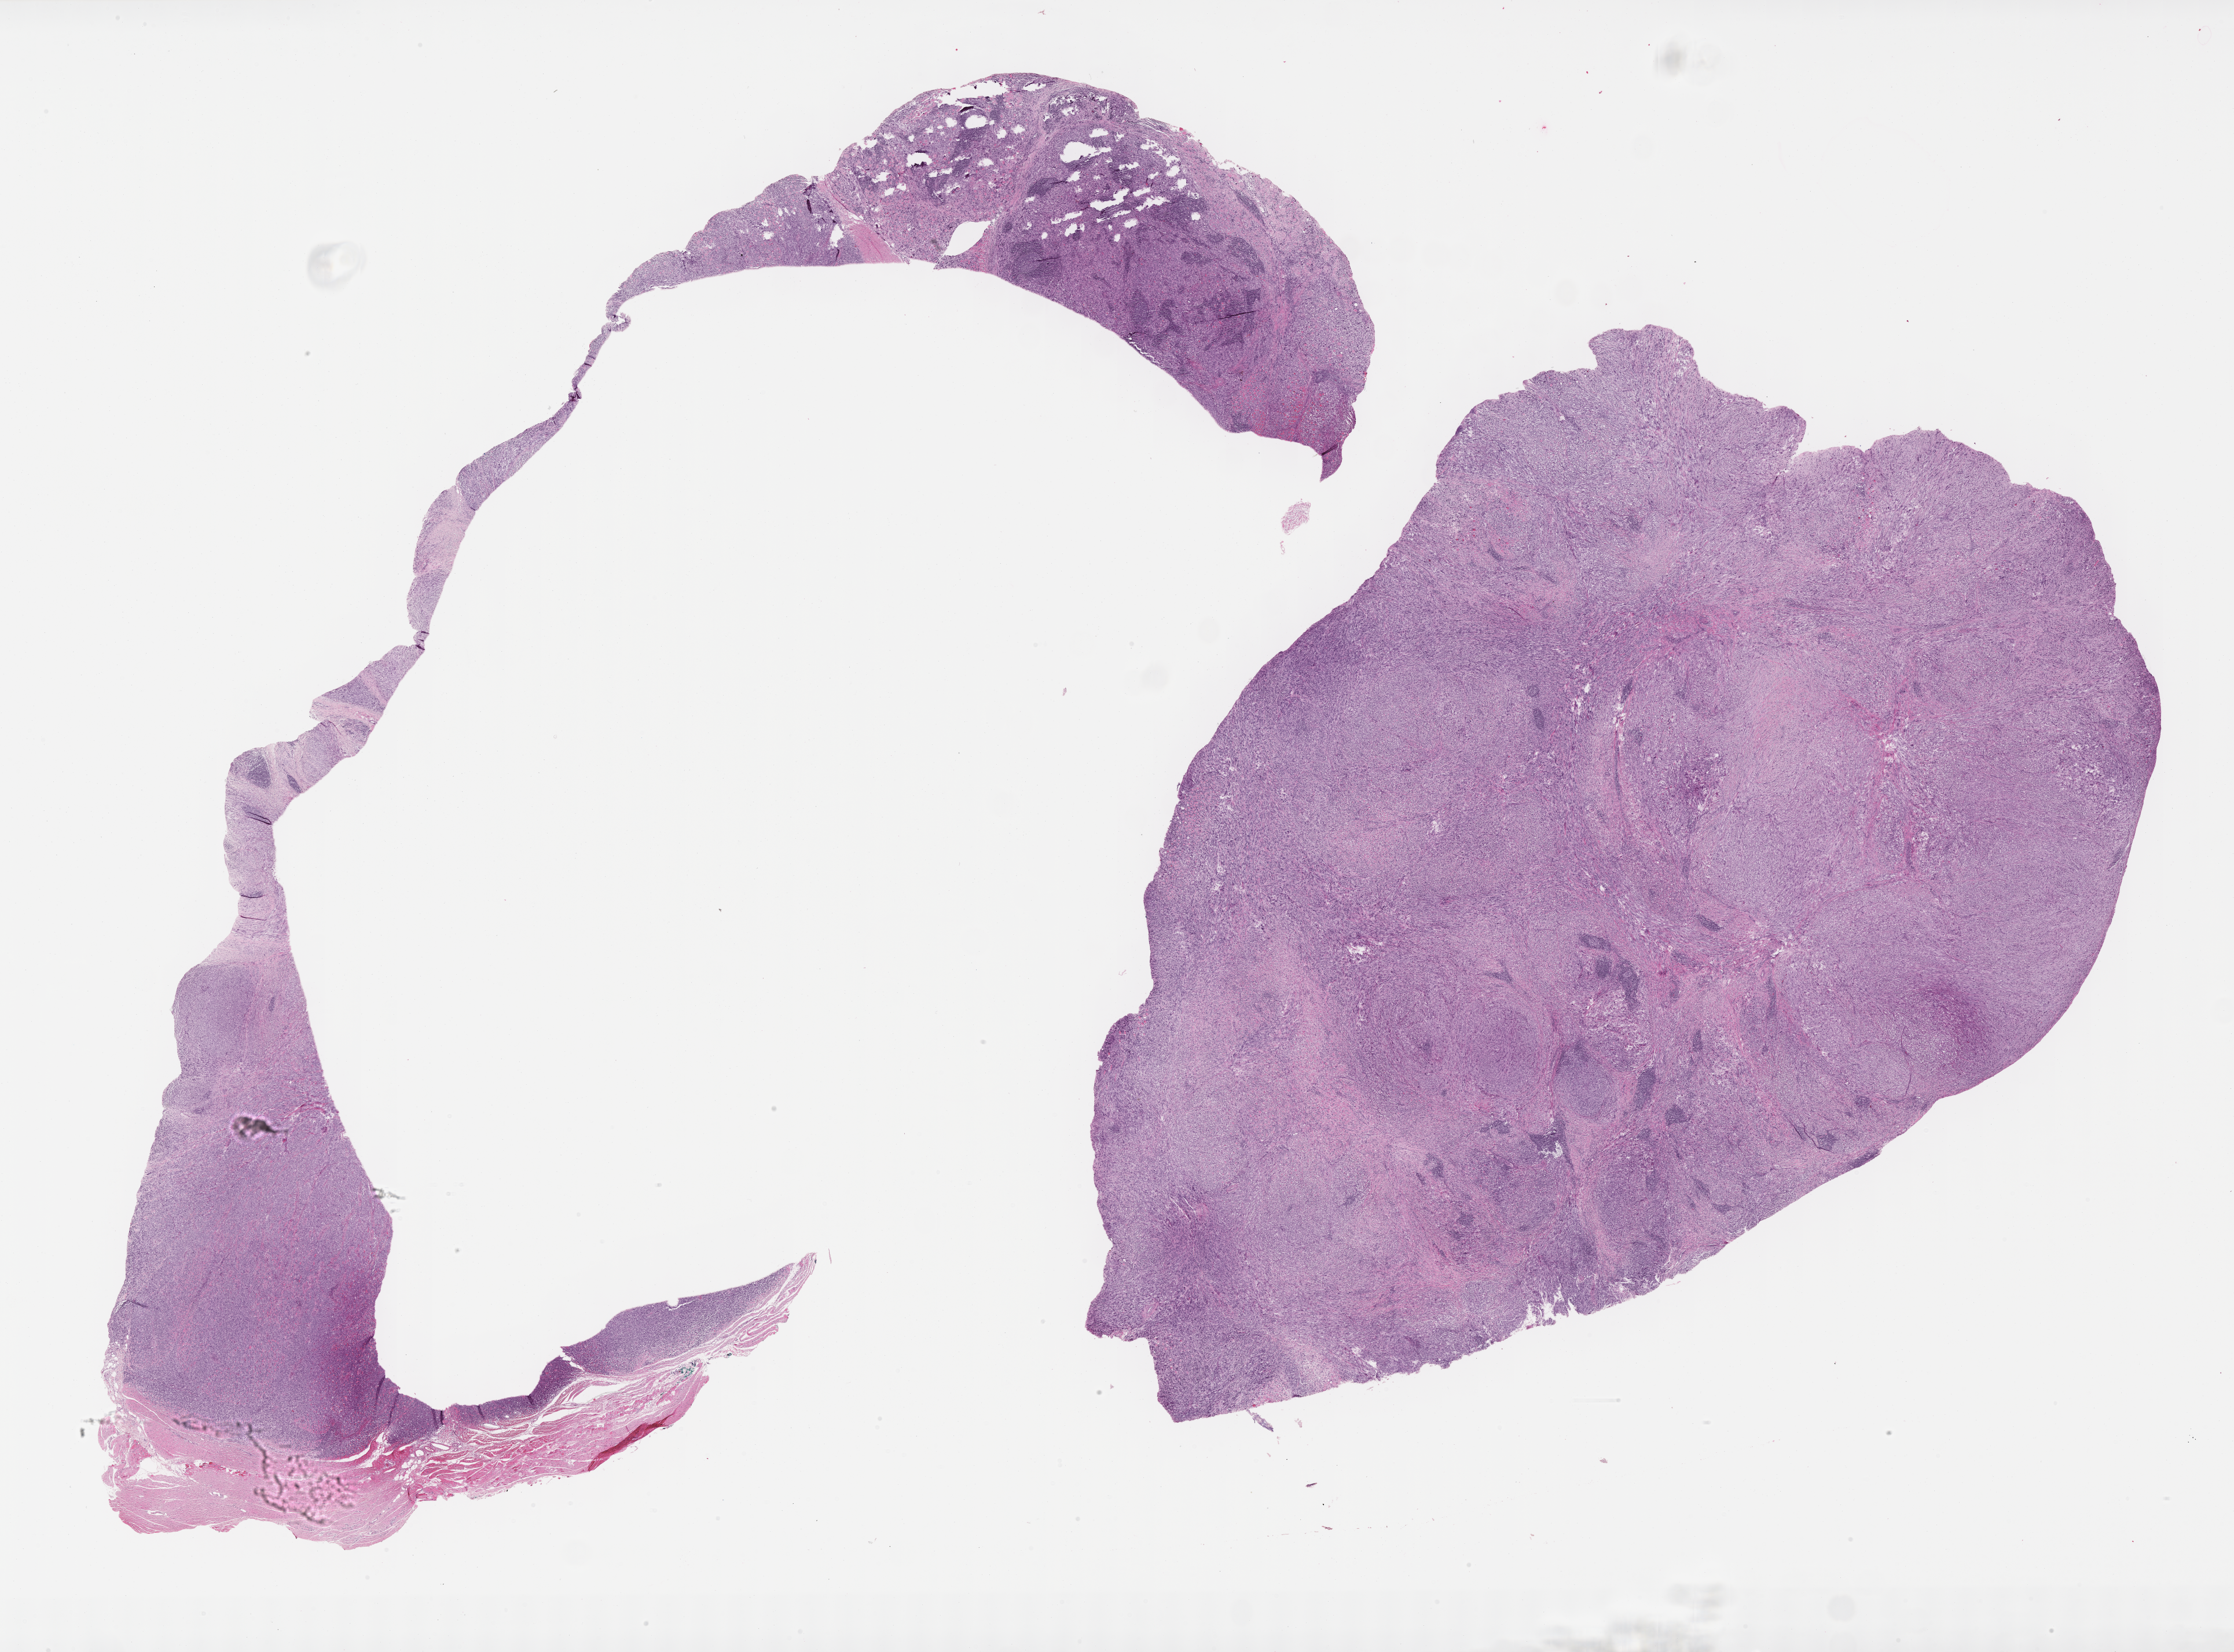
Haematoxylin and eosin whole-slide image of tumor tissue — a low-resolution overview of the entire scanned area, about 31.2 x 23.1 mm; formalin-fixed, paraffin-embedded (FFPE) tissue. Patient: female, age 3.1 years at diagnosis.
Diagnosis: rhabdomyosarcoma; histological classification: spindle cell rhabdomyosarcoma.